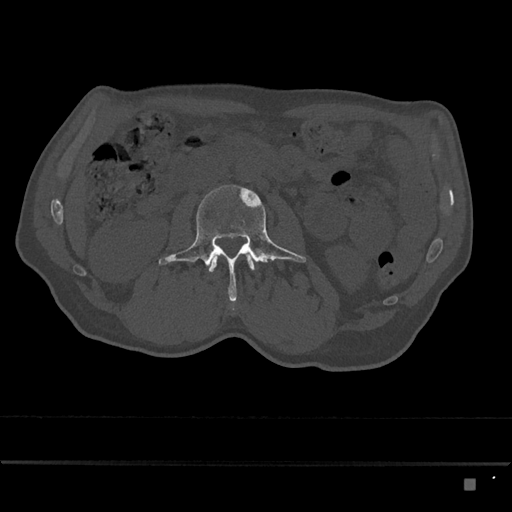
CT including the spine, one axial slice. 120 kVp. Bone window (W 1800 / L 400 HU). 0.5 mm slice thickness. 512 × 512 image matrix, field of view 390 × 390 mm. Patient: male, 72 years. From the clinical record (not read from this slice): primary cancer: prostate.
Annotated regions visible in this slice (semi-automatically segmented with operator editing):
- L2 vertebra: bounding box [x1, y1, x2, y2] px = [208, 255, 256, 273]
- L3 vertebra: [159, 185, 306, 302]